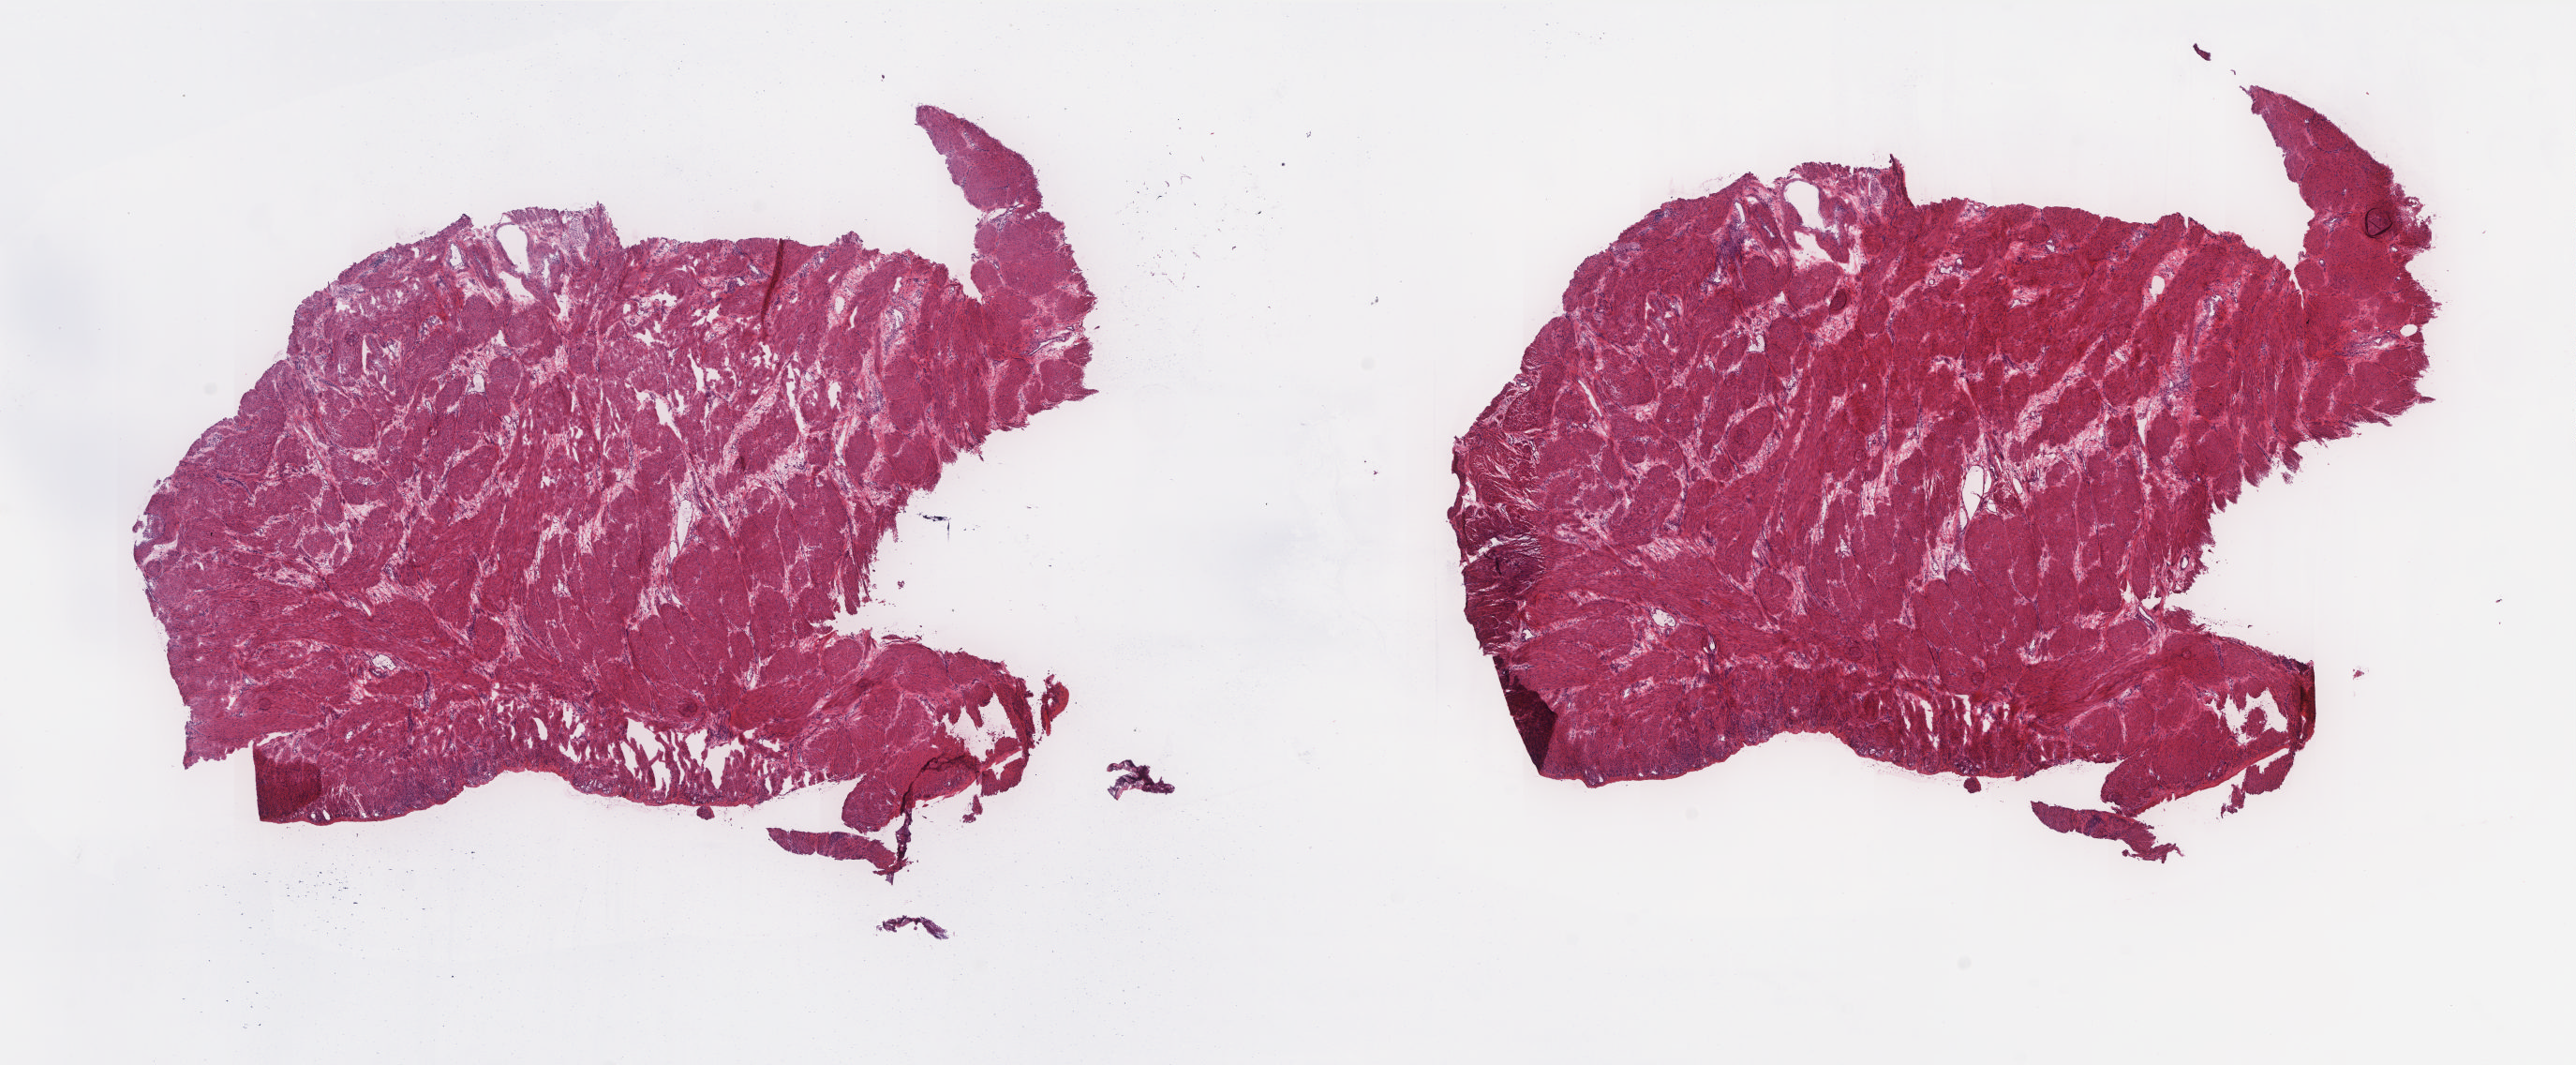
H&E-stained whole-slide image — shown as a low-resolution overview of the whole scanned area (about 22.0 x 9.1 mm). Frozen section from the top of the tissue portion. Solid tissue normal (non-tumour tissue) sample from the uterus. Female patient; age at initial diagnosis 60 years. Slide review estimates, as recorded: tumour cells 0%, normal cells 100%. Infiltration values recorded for this section: lymphocyte infiltration 5%, monocyte infiltration 0%, neutrophil infiltration 0%.
This section: solid tissue normal (non-tumour) sample from the same patient. Patient diagnosis: Endometrioid adenocarcinoma, NOS (endometrium).